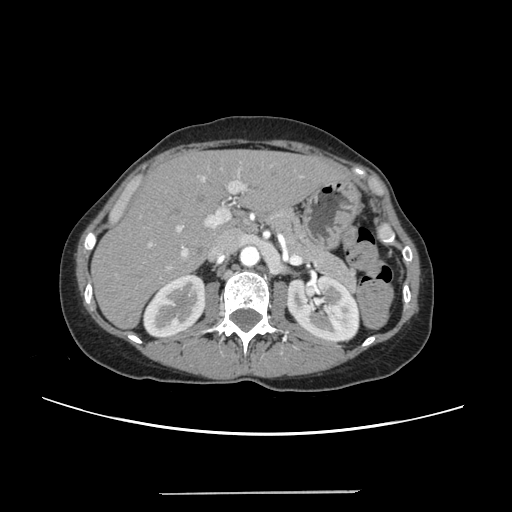
Contrast-enhanced abdominal CT, one axial slice. Position 143 of 240 along the scan axis. Intravenous contrast given. Soft-tissue window (W 400 / L 40 HU). 1.25 mm slice thickness. 512 × 512 image matrix. Female patient, age 60 years. Case-level facts recorded for this patient, not image findings: diagnosis: colorectal cancer liver metastases, imaged before liver resection; multiple liver metastases: no; largest metastasis: 1.5 cm; disease in both lobes: no.
Outlined on this slice (manually delineated by an expert):
- liver: bounding box <94,151,344,327> (left, top, right, bottom; pixels)
- planned liver remnant (the part of the liver to remain after resection): <94,151,344,326>
- portal vein (with intrahepatic branches): <143,168,254,269>